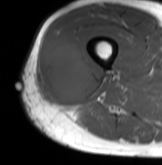
MRI of an extremity soft-tissue mass, one axial slice; slice 32 of 61 in the series (ordered by position); MR volume resampled by the dataset authors to the PET/CT grid (not the native acquisition matrix); 3.27 mm slice thickness; 162 × 165 image matrix. Male patient. Case-level facts recorded for this patient, not image findings: histological type: poorly differentiated synovial sarcoma; grade: high; site of the primary tumour: right buttock.
Structures marked on this image (expert contour drawn on MRI and transferred to this co-registered scan by the dataset authors):
- gross tumour volume including surrounding oedema: bounding box <36,33,95,103> (left, top, right, bottom; pixels)
- gross tumour volume (mass): <43,38,95,103>